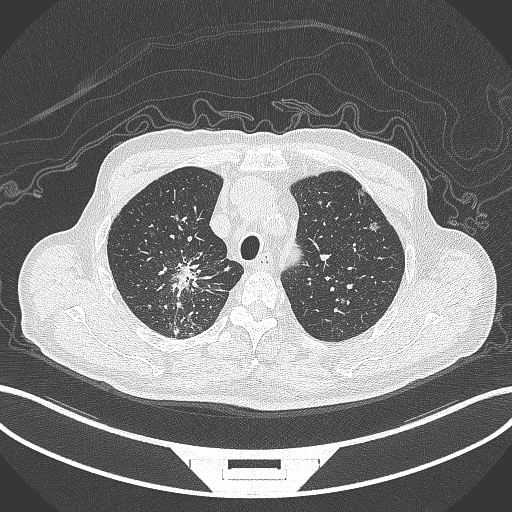
Chest CT, one axial slice. Slice 300 of 407 in the series (ordered by position). Reconstruction kernel B70f. 120 kVp. Lung window (W 1500 / L -600 HU). 1 mm slice thickness. 512 × 512 image matrix, field of view 400 × 400 mm. Male patient, age 69 years. Case-level facts recorded for this patient, not image findings: clinical TNM (as recorded): T1c N1 M1.
Annotated regions visible in this slice (bounding box drawn by a radiologist):
- lung tumour (recorded histology: adenocarcinoma): bounding box (x1, y1, x2, y2) in pixels: (169, 256, 208, 303)